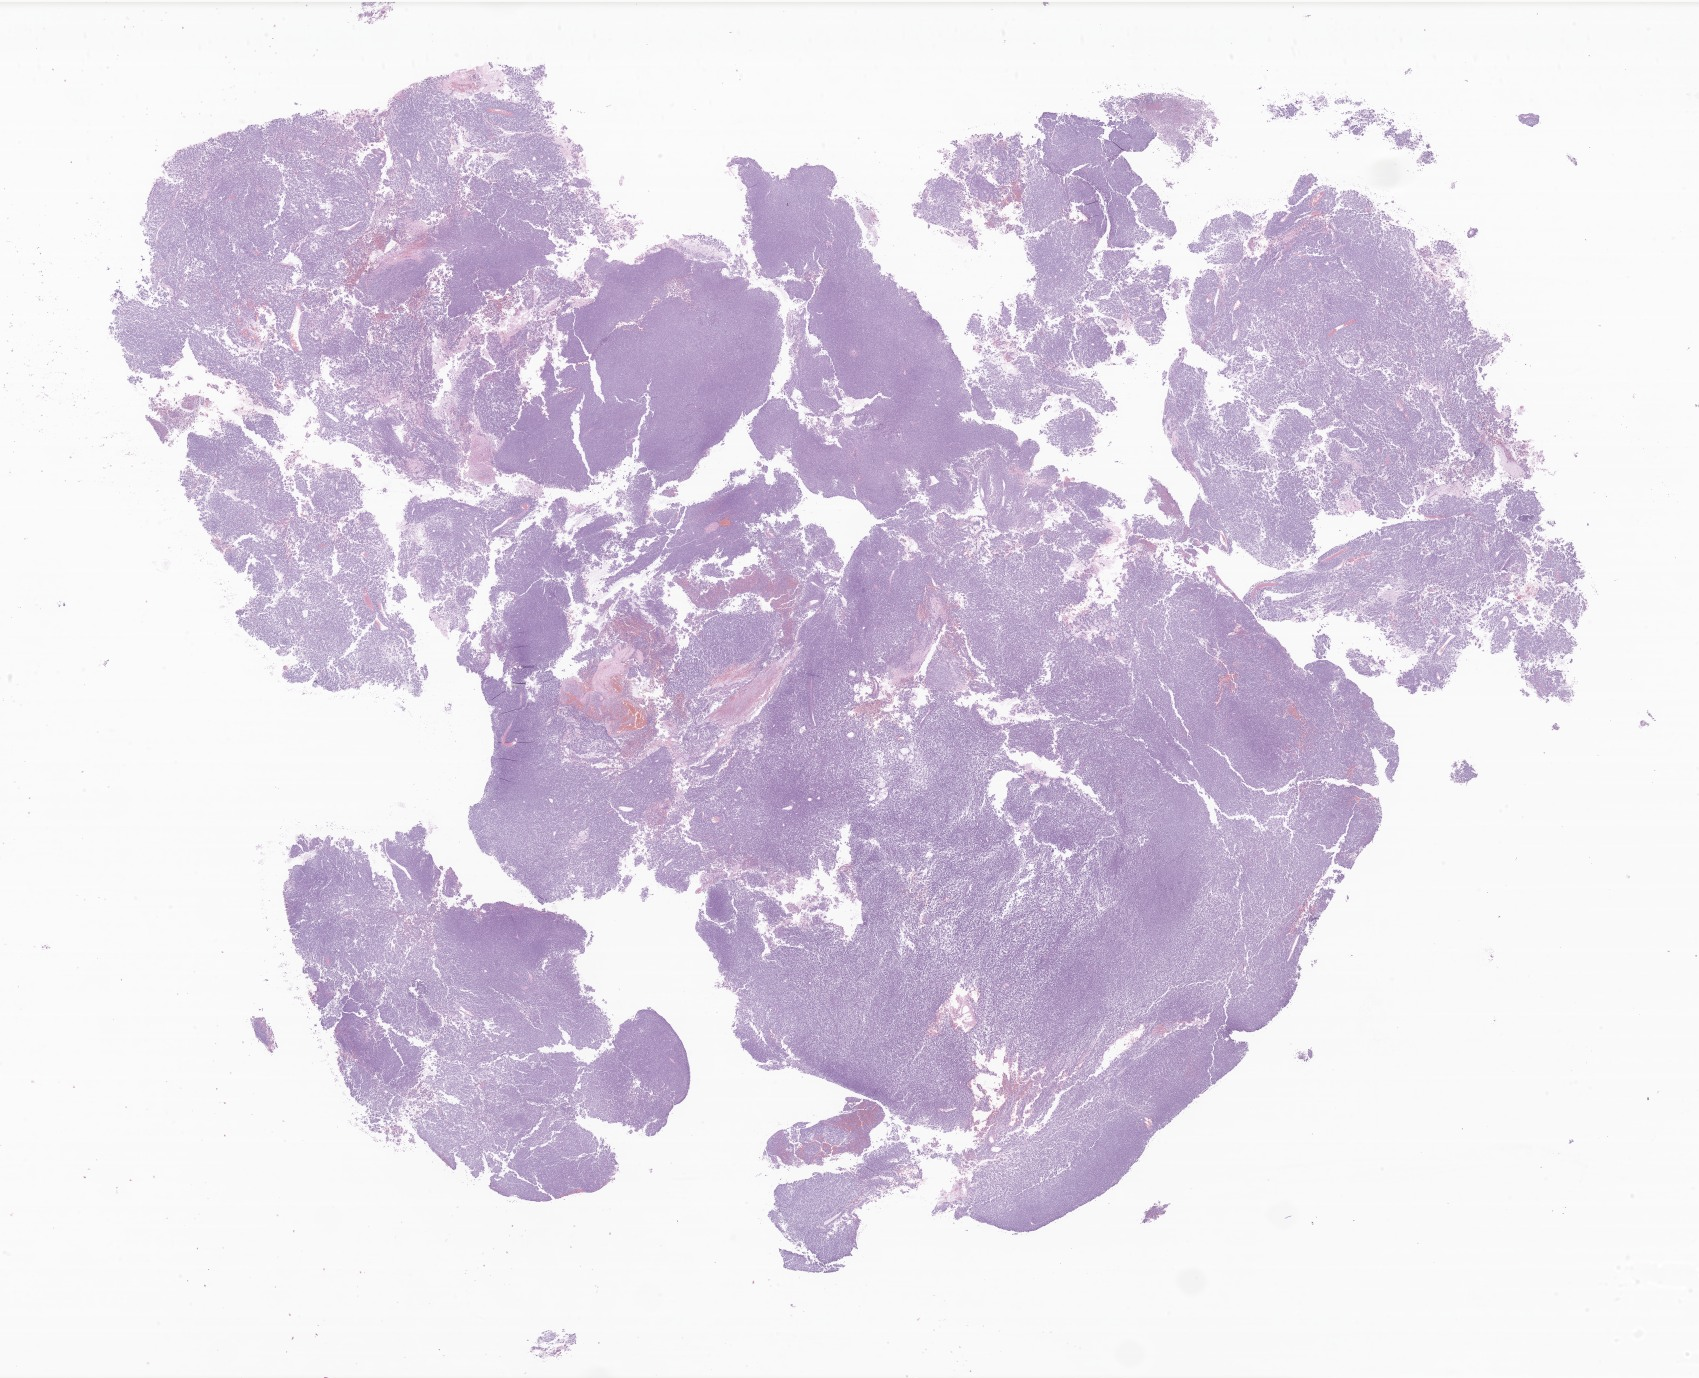
Digitized H&E-stained section of tumor tissue from the pelvis, a low-resolution overview of the entire scanned area, about 28.7 x 23.2 mm; FFPE section. Patient: male, age 846 days (about 2.3 years).
• recorded diagnosis: Rhabdoid tumor, NOS